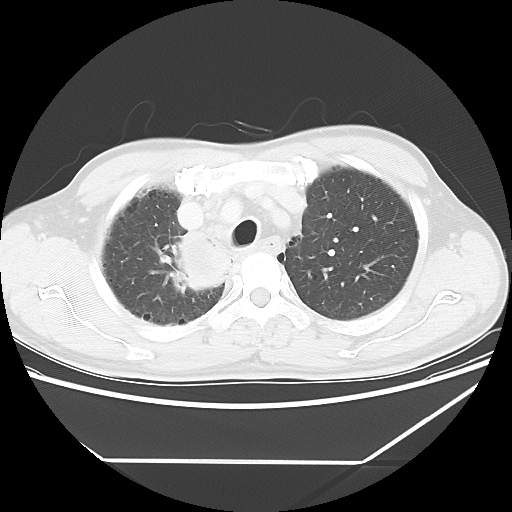
Chest CT, one axial slice; position 48 of 60 along the scan axis; reconstruction kernel LUNG; 120 kVp; lung window (W 1500 / L -600 HU); 5 mm slice thickness; 512 × 512 image matrix, field of view 367 × 367 mm. Patient: male, 58 years. From the clinical record (not read from this slice): clinical TNM (as recorded): T2 N2 M0.
Structures marked on this image (rectangle marked by the reading radiologist):
- lung tumour (recorded histology: squamous cell carcinoma): box from (x=157, y=226) to (x=234, y=307) px